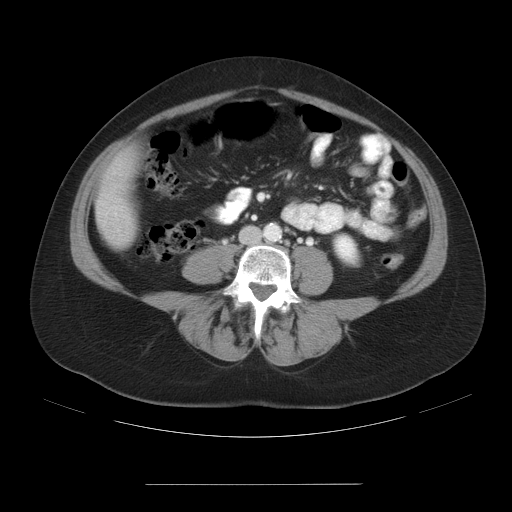
Contrast-enhanced abdominal CT, one axial slice. Slice 3 of 27 in the series (ordered by position). Reconstruction kernel STANDARD. Intravenous contrast given. Soft-tissue window (W 400 / L 40 HU). 7.5 mm slice thickness. 512 × 512 image matrix, field of view 440 × 440 mm. Female patient, age 58 years. Case-level facts recorded for this patient, not image findings: diagnosis: colorectal cancer liver metastases, imaged before liver resection; multiple liver metastases: yes; largest metastasis: 1.9 cm.
Structures marked on this image (outlined manually by an expert reader):
- liver: bounding box (x1, y1, x2, y2) in pixels: (97, 155, 137, 247)
- planned liver remnant (the part of the liver to remain after resection): (113, 155, 135, 177)